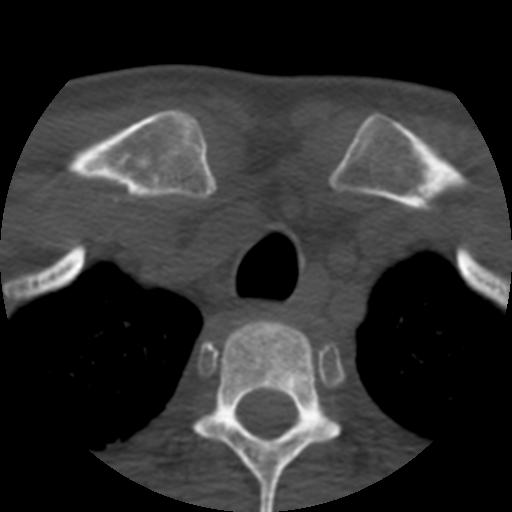
CT including the spine, one axial slice. Slice 431 of 508 in the series (ordered by position). 120 kVp. Bone window (W 1800 / L 400 HU). 1.25 mm slice thickness. 512 × 512 image matrix, field of view 160 × 160 mm. Patient age 57 years. From the clinical record (not read from this slice): primary cancer: prostate.
Annotated regions visible in this slice (semi-automatic segmentation, software-assisted and operator-edited):
- T2 vertebra: bounding box (x1, y1, x2, y2) in pixels: (195, 320, 339, 512)
- T3 vertebra: (329, 419, 331, 421)